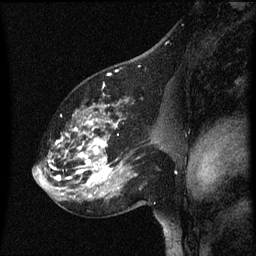
Breast MRI (dynamic contrast-enhanced), one sagittal slice; position 36 of 60 along the scan axis; dynamic contrast-enhanced series, image 2 of 3 at this slice position (ordered by acquisition); 1.5 T; TE 4.2 ms, TR 8 ms; 2 mm slice thickness; 256 × 256 image matrix, field of view 200 × 200 mm. Patient: female, 60 years.
Annotated regions visible in this slice (semi-automatically segmented with operator editing):
- analysis volume of interest (the breast-tissue region the enhancement analysis was run in; not a lesion): bounding box [x1, y1, x2, y2] px = [49, 98, 158, 197]
- tumour enhancement mask (voxels above the 70 % enhancement threshold inside the analysis volume of interest): [51, 120, 120, 189]